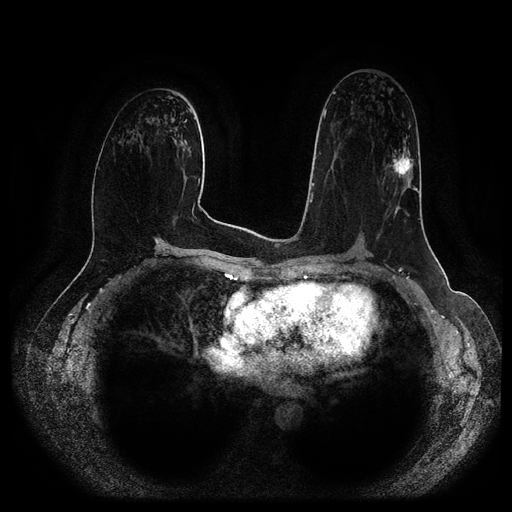
Breast MRI (dynamic contrast-enhanced, multi-phase), one axial slice; slice 56 of 116 in the series (ordered by position); dynamic contrast-enhanced series, time point 2 of 5 at this slice position (early post-contrast); 1.5 T; TE 2.6 ms, TR 5.2 ms; 2 mm slice thickness; 512 × 512 image matrix, field of view 380 × 380 mm. Female patient, age 57 years.
Annotated regions visible in this slice (semi-automatically segmented with operator editing):
- breast lesion (labelled 'tumour' in the annotation; benign lesions carry a separate 'benign' label): bounding box (x1, y1, x2, y2) in pixels: (389, 150, 415, 178)